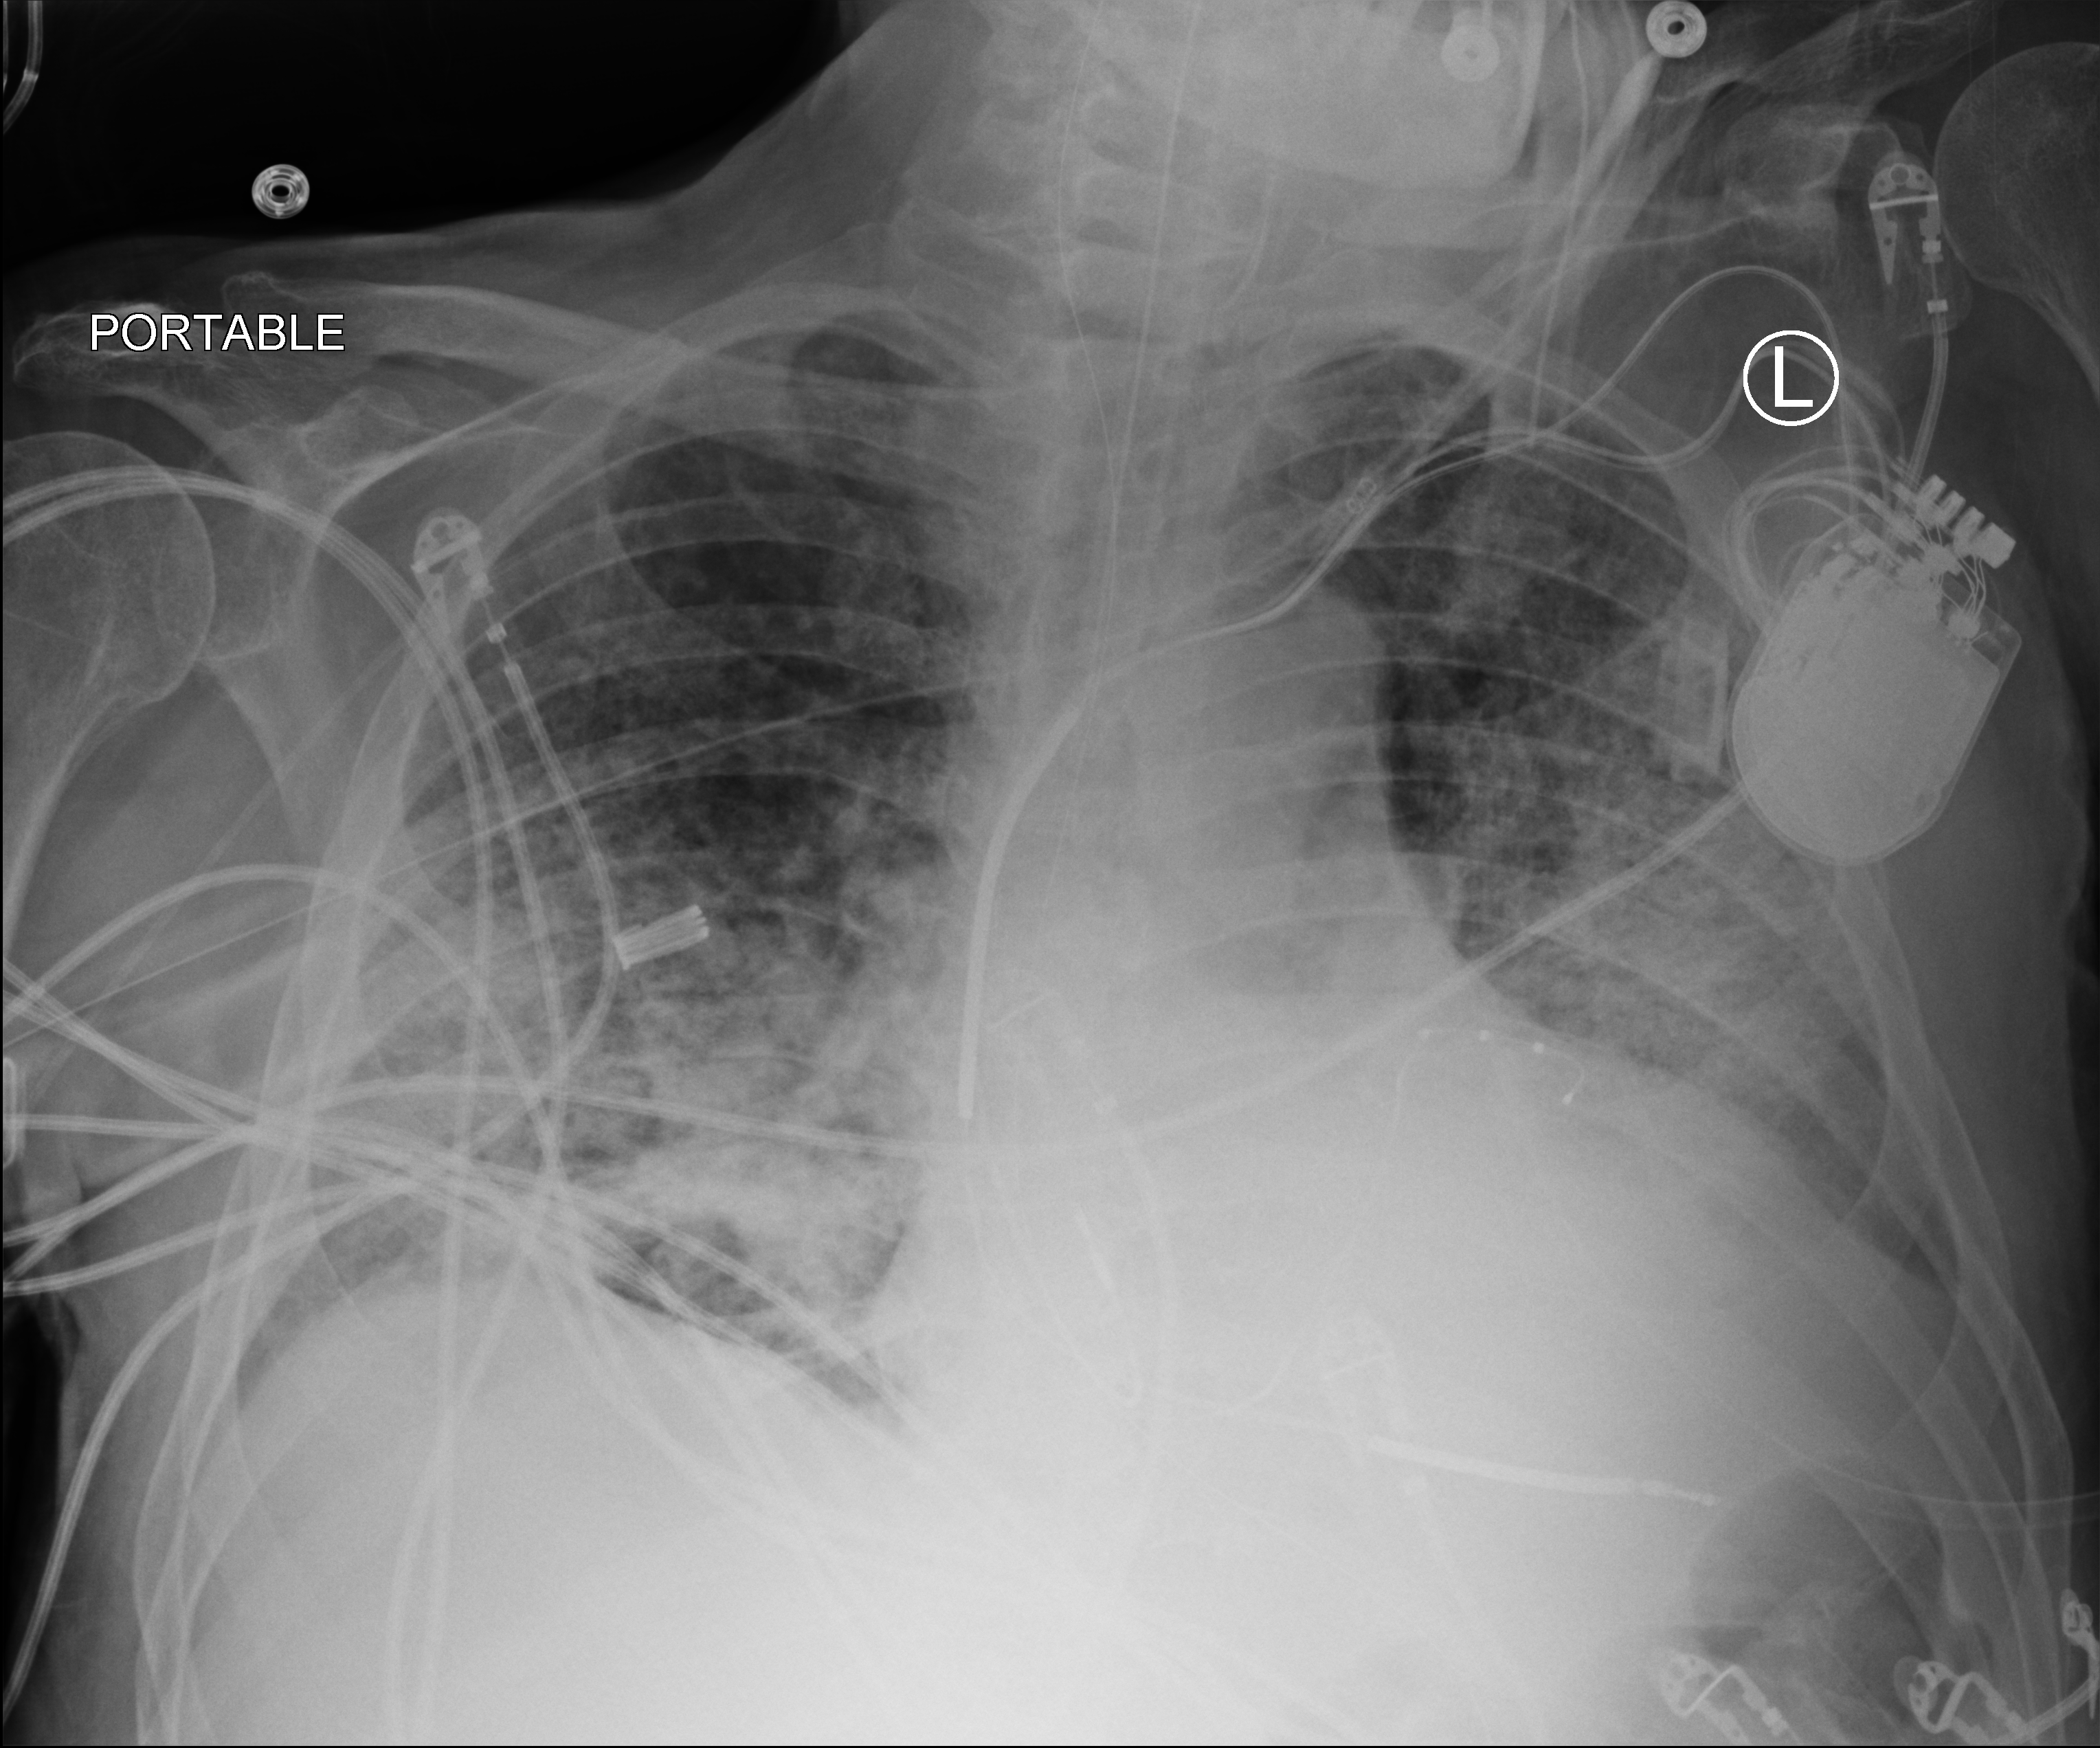
Portable chest radiograph; anteroposterior (AP) projection. Male patient hospitalised with COVID-19, age 60–74 years.
From the hospital-stay record, not from the radiograph (when in the stay this image was taken is not recorded): length of hospital stay: 36 days.